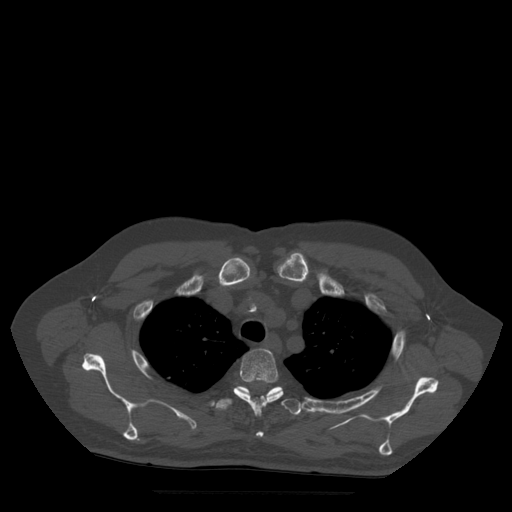
CT including the spine, one axial slice; slice 404 of 522 in the series (ordered by position); bone window (W 1800 / L 400 HU); 1.25 mm slice thickness; 512 × 512 image matrix, field of view 420 × 420 mm. Patient age 72 years. Case-level facts recorded for this patient, not image findings: primary cancer: prostate.
Annotated regions visible in this slice (semi-automatically segmented with operator editing):
- T3 vertebra: bounding box <234,349,284,438> (left, top, right, bottom; pixels)
- T4 vertebra: <216,387,302,416>